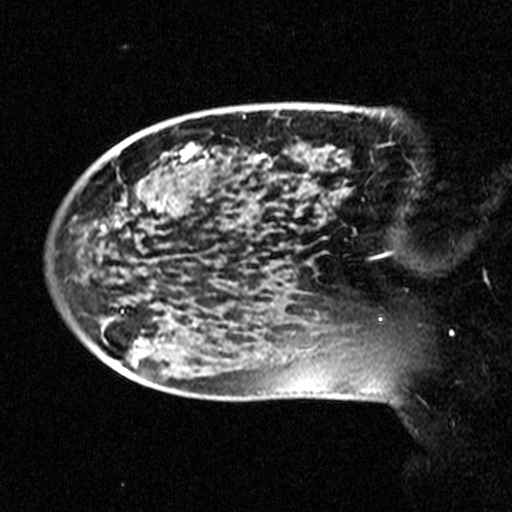
Breast MRI (dynamic contrast-enhanced), one sagittal slice. Position 10 of 44 along the scan axis. Dynamic contrast-enhanced study with each time point stored as its own series, time point 2 of 3 at this slice position (early post-contrast, ordered by acquisition time). 1.5 T. TE 4.5 ms, TR 11 ms. 3 mm slice thickness. 512 × 512 image matrix, field of view 240 × 240 mm. Female patient, age 38 years. Case-level facts recorded for this patient, not image findings: setting: breast cancer imaged before/during neoadjuvant chemotherapy; receptor status: HR-positive, HER2-negative.
Structures marked on this image (semi-automatically segmented with operator editing):
- analysis volume of interest (the breast-tissue region the enhancement analysis was run in; not a lesion): bounding box <124,106,405,245> (left, top, right, bottom; pixels)
- tumour enhancement mask (voxels above the 90 % enhancement threshold inside the analysis volume of interest): <184,143,394,171>